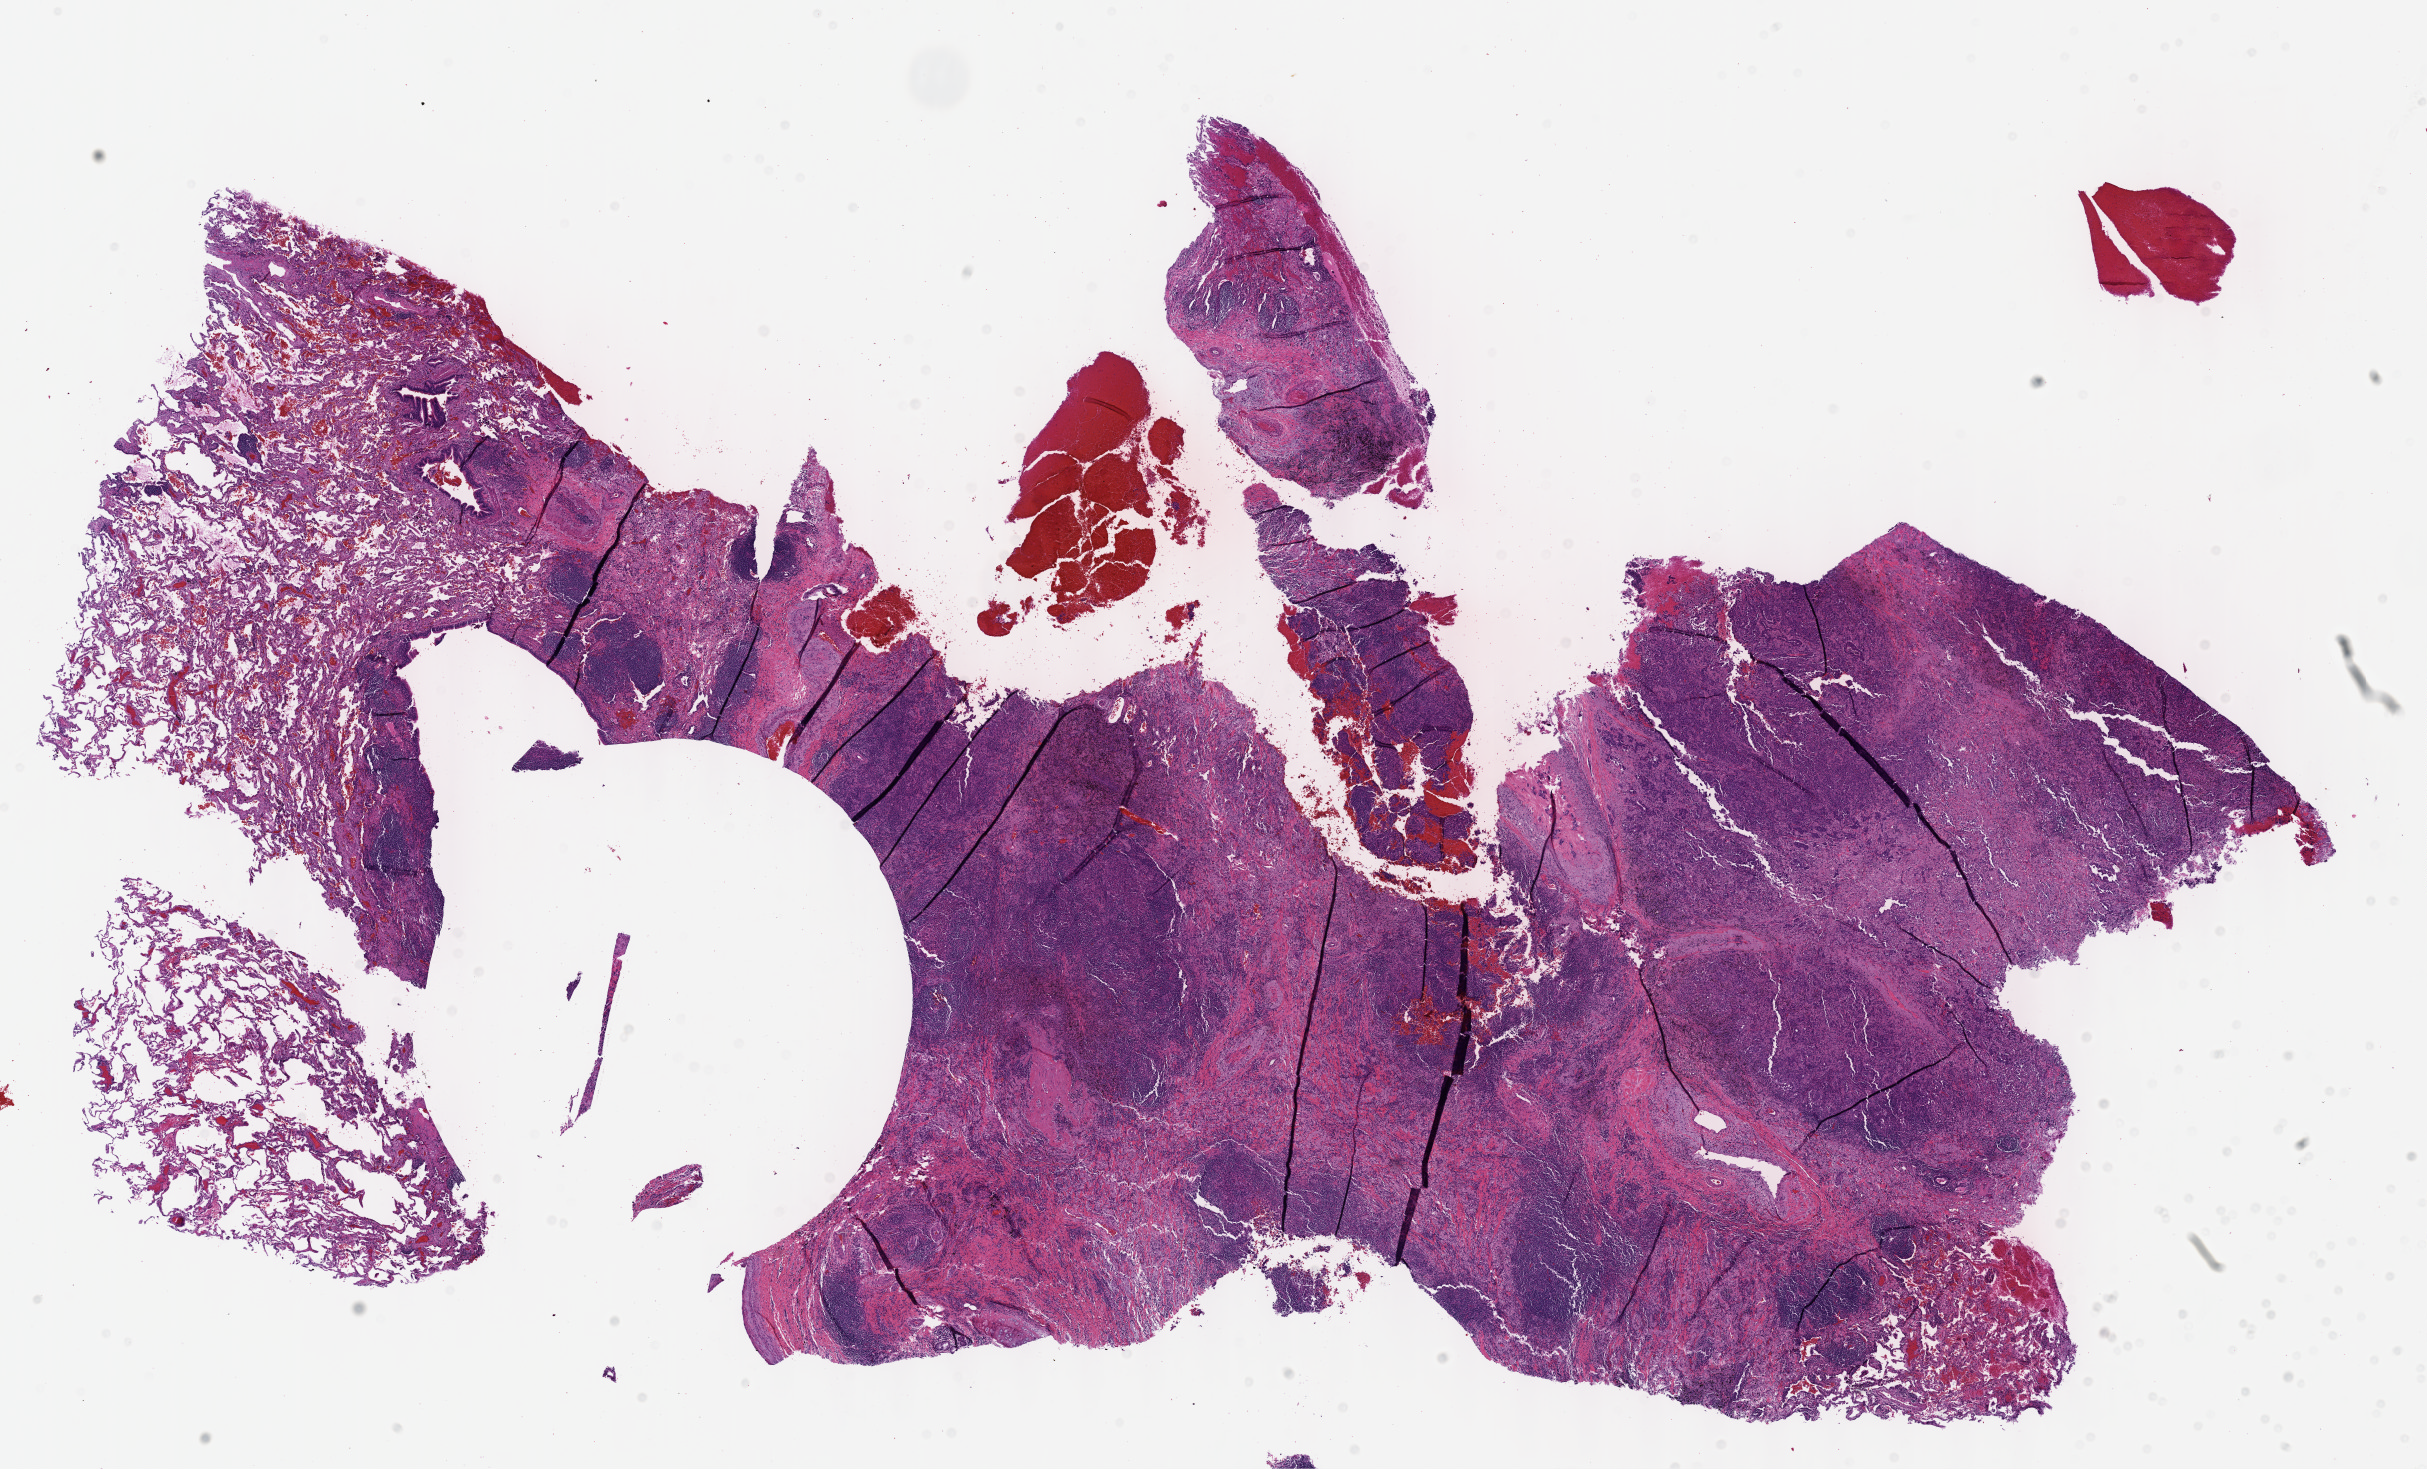
H&E whole-slide image, a low-resolution overview of the entire scanned area, about 19.6 x 11.9 mm (from a 40x scan). Formalin-fixed paraffin-embedded (FFPE) diagnostic section. Sample: primary tumour, lung. Male, age 69 years at initial diagnosis.
AJCC pathologic stage: IIB (6th edition). Histologic diagnosis: Adenocarcinoma, NOS (upper lobe, lung).